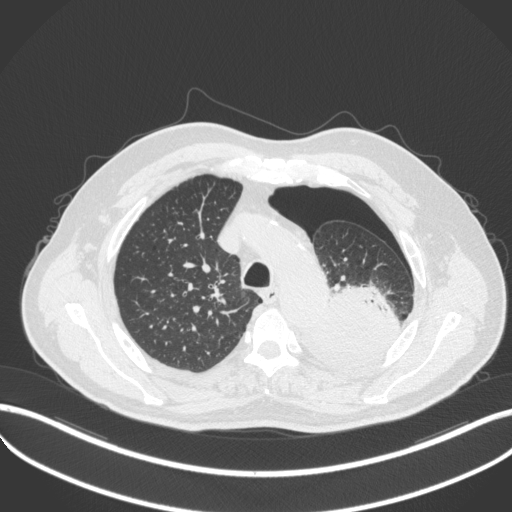
Chest CT, one axial slice. Slice 385 of 466 in the series (ordered by position). 120 kVp. Lung window (W 1500 / L -600 HU). 1 mm slice thickness. 512 × 512 image matrix, field of view 400 × 400 mm. Patient: male, 76 years. Case-level facts recorded for this patient, not image findings: clinical TNM (as recorded): T3 N0 M1b.
Annotated regions visible in this slice (rectangle marked by the reading radiologist):
- lung tumour (recorded histology: adenocarcinoma): bounding box <300,282,398,371> (left, top, right, bottom; pixels)